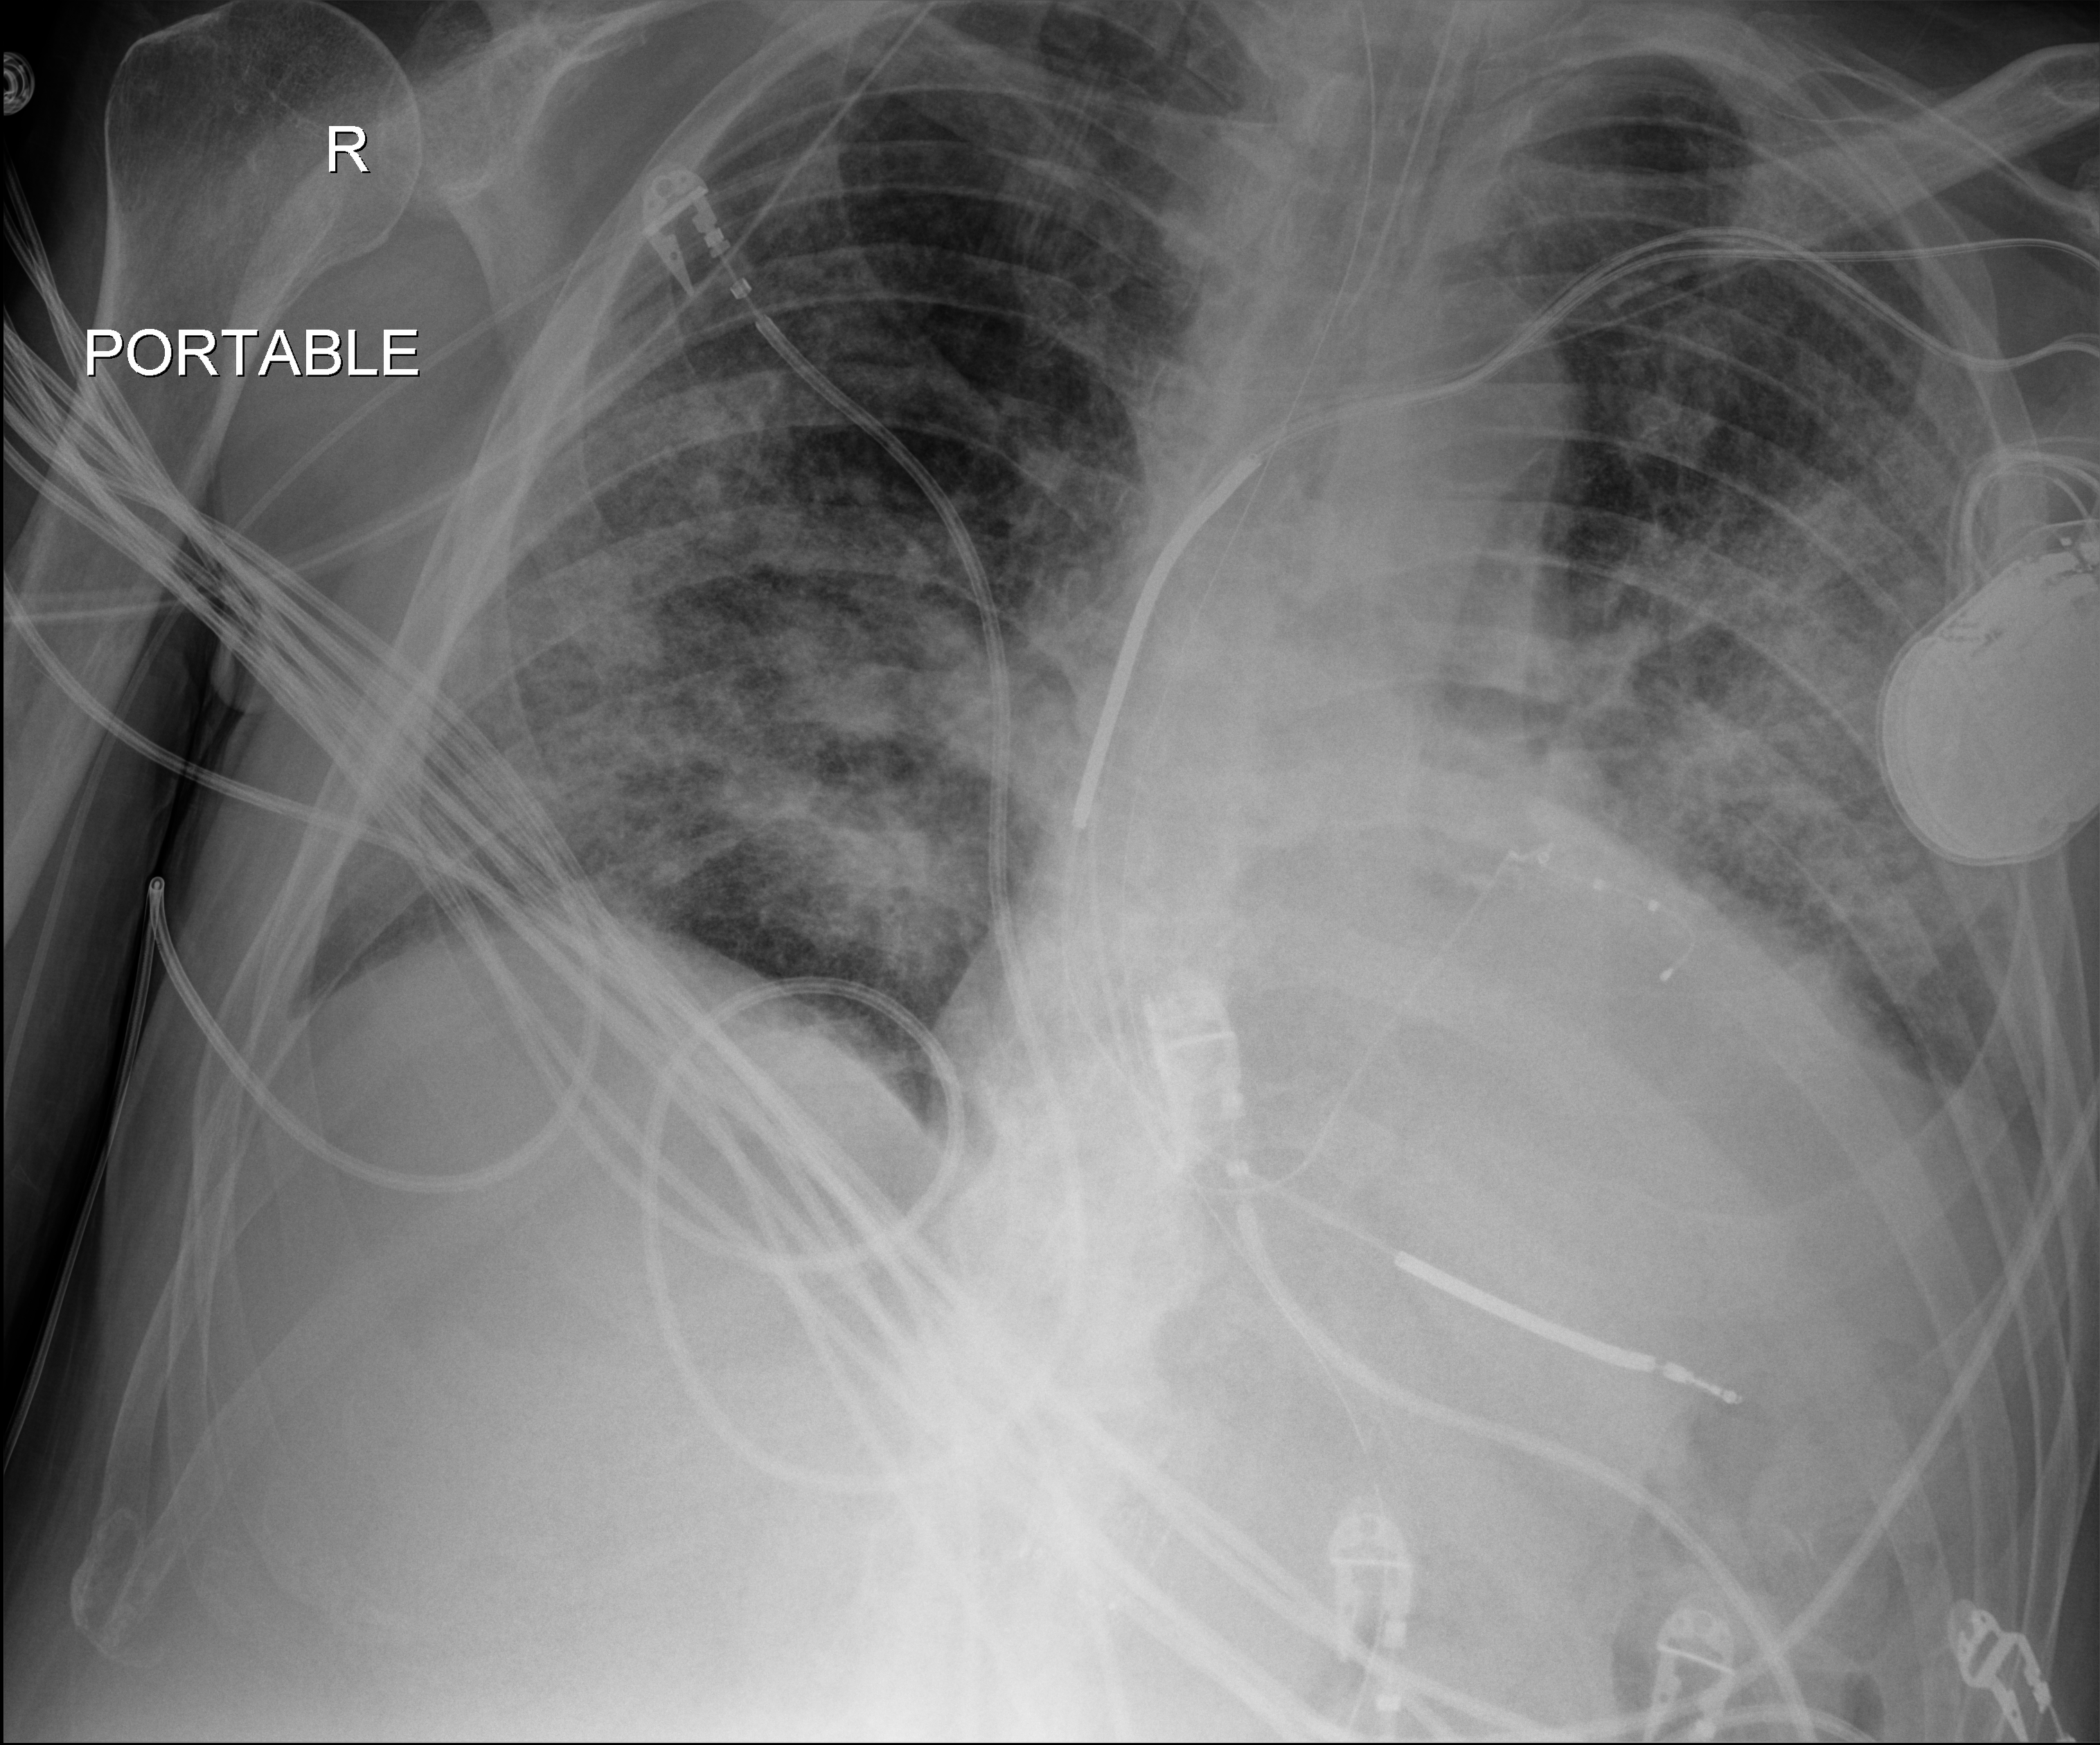
Portable chest radiograph; anteroposterior (AP) projection. Patient hospitalised with COVID-19; male, aged 60–74 years.
Hospital-stay facts (about this admission, not read from this image; timing relative to this image not recorded):
- mechanically ventilated during this hospital stay: yes
- smoking status (admission record): former